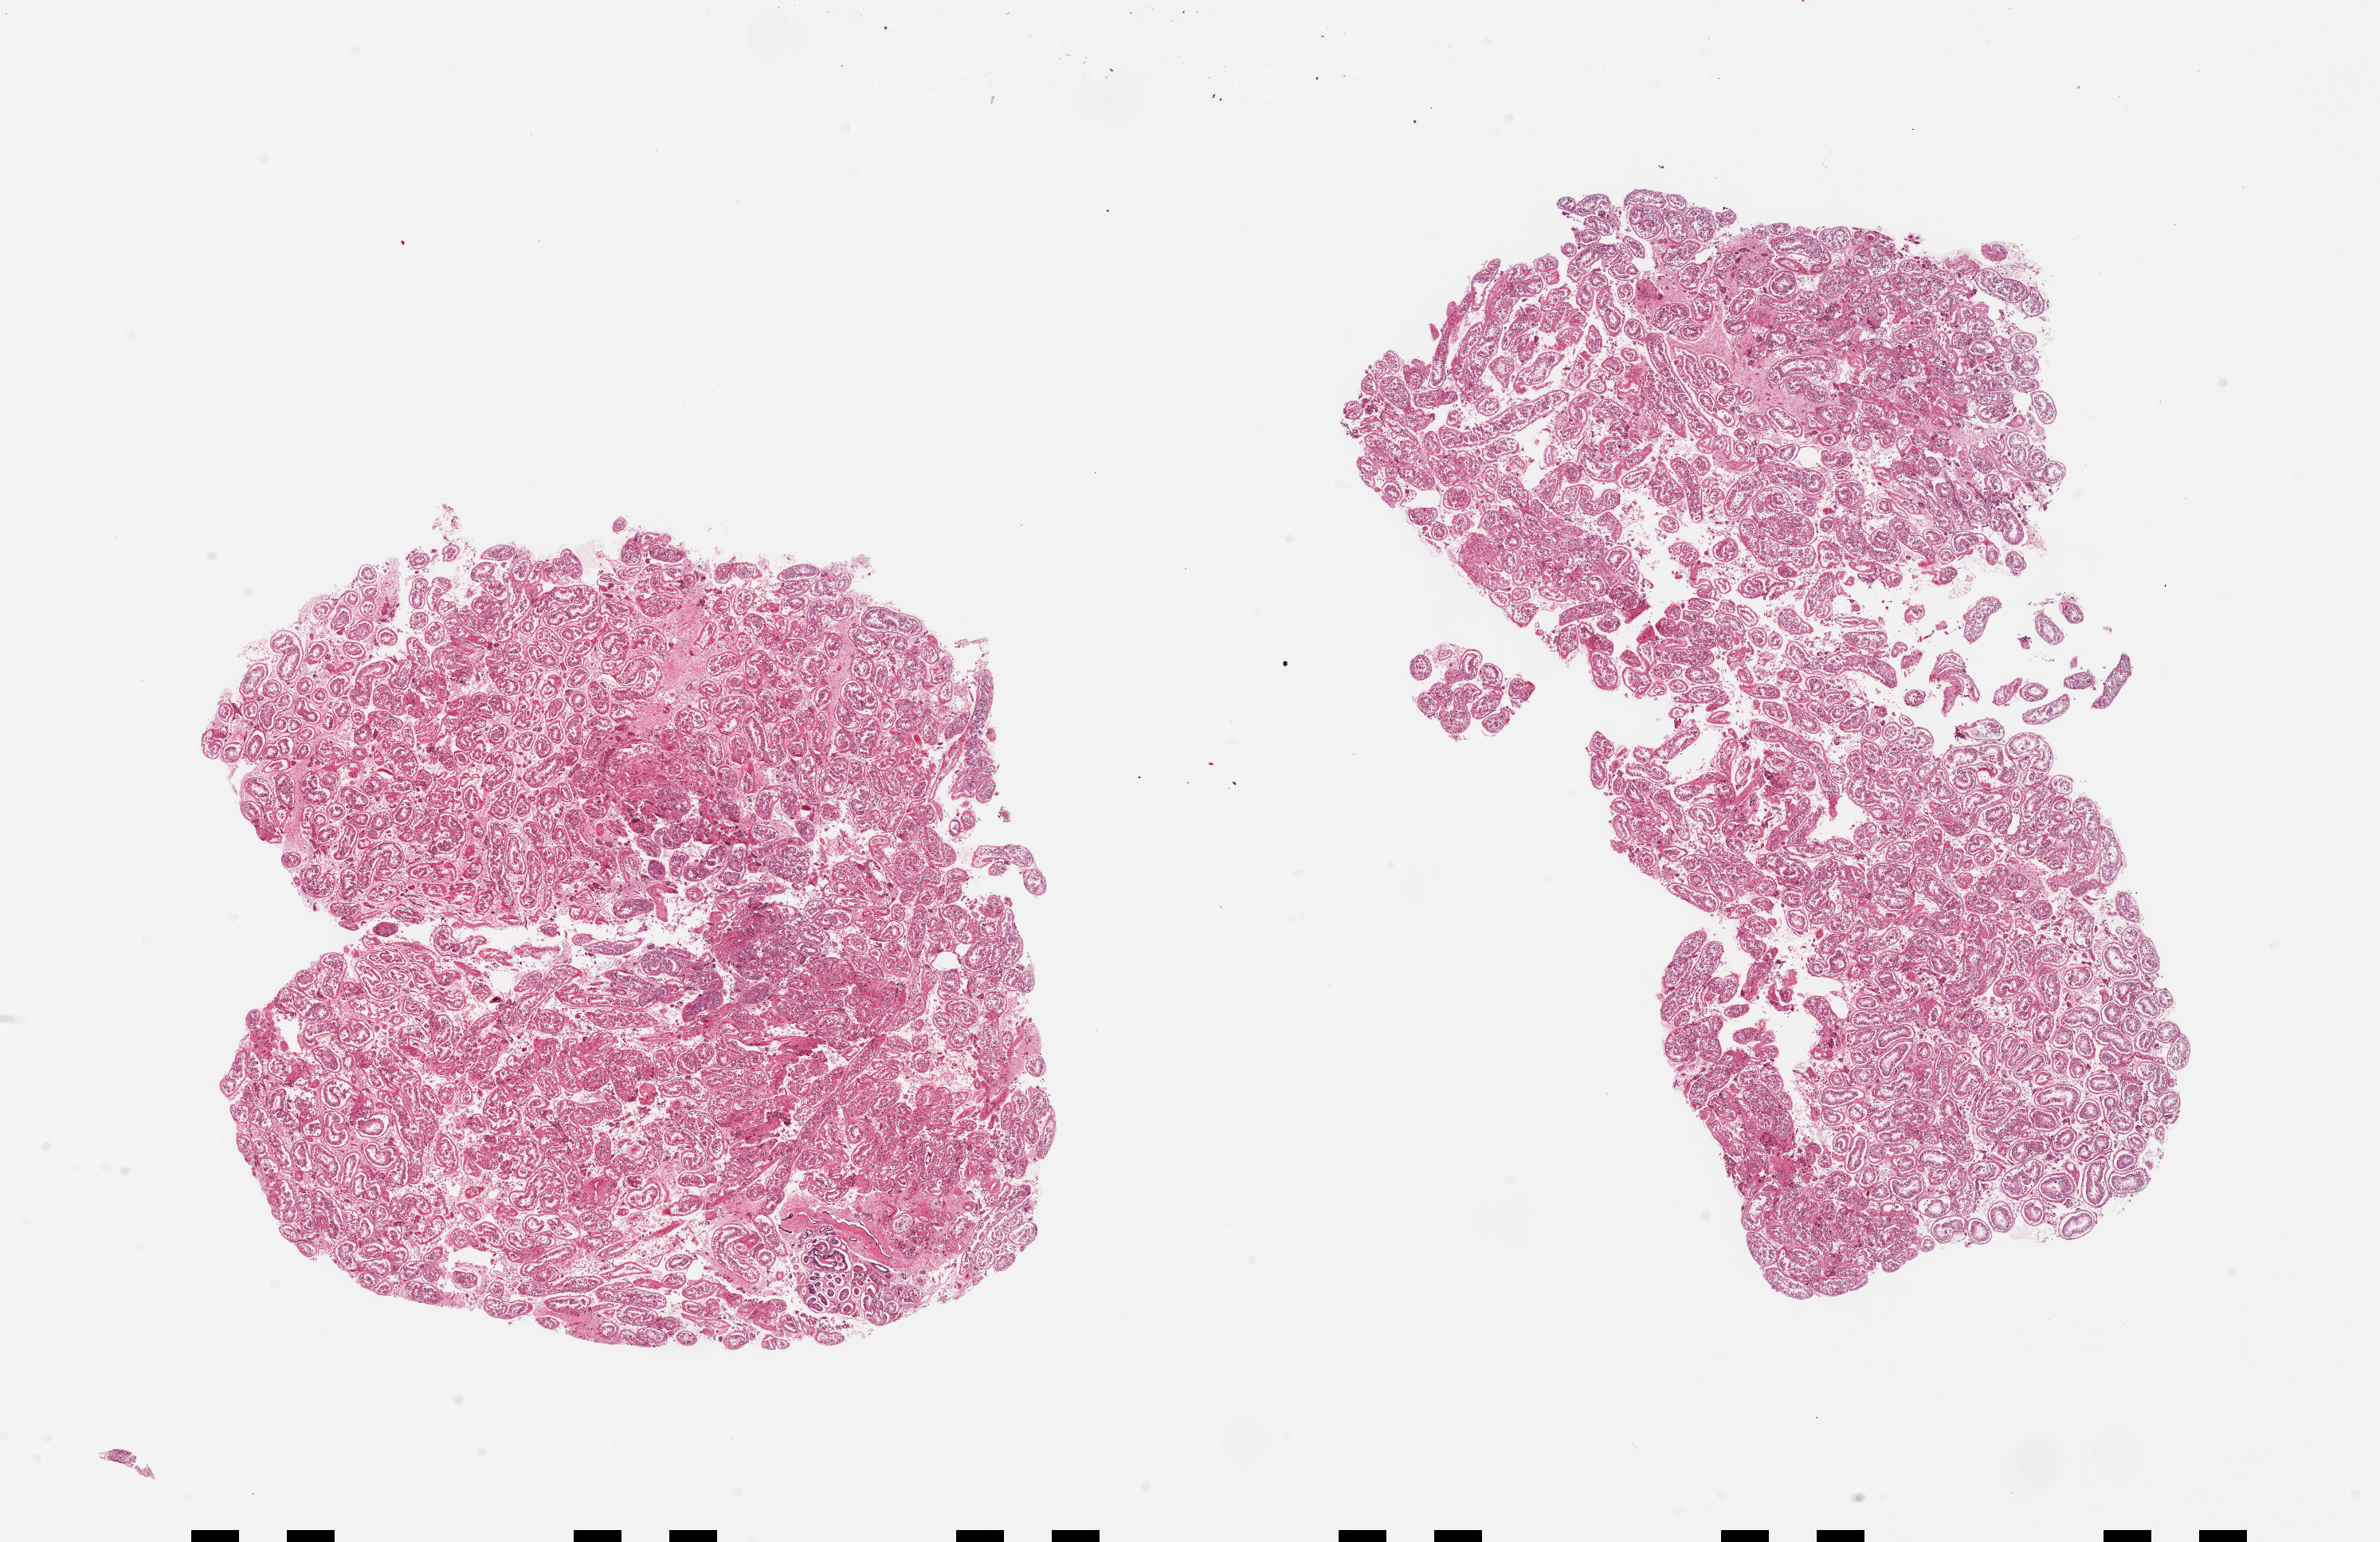
Whole-slide image, haematoxylin and eosin stain, brightfield — low-resolution overview of the scanned area, about 23.6 x 15.3 mm; PAXgene-fixed paraffin-embedded (PFPE) section; sampled site (target tissue): testis; donor tissue sample. Donor: male.
Reviewer comment on this tissue sample: 2 pieces, autolysis precludes assessment of spermatogenesis.